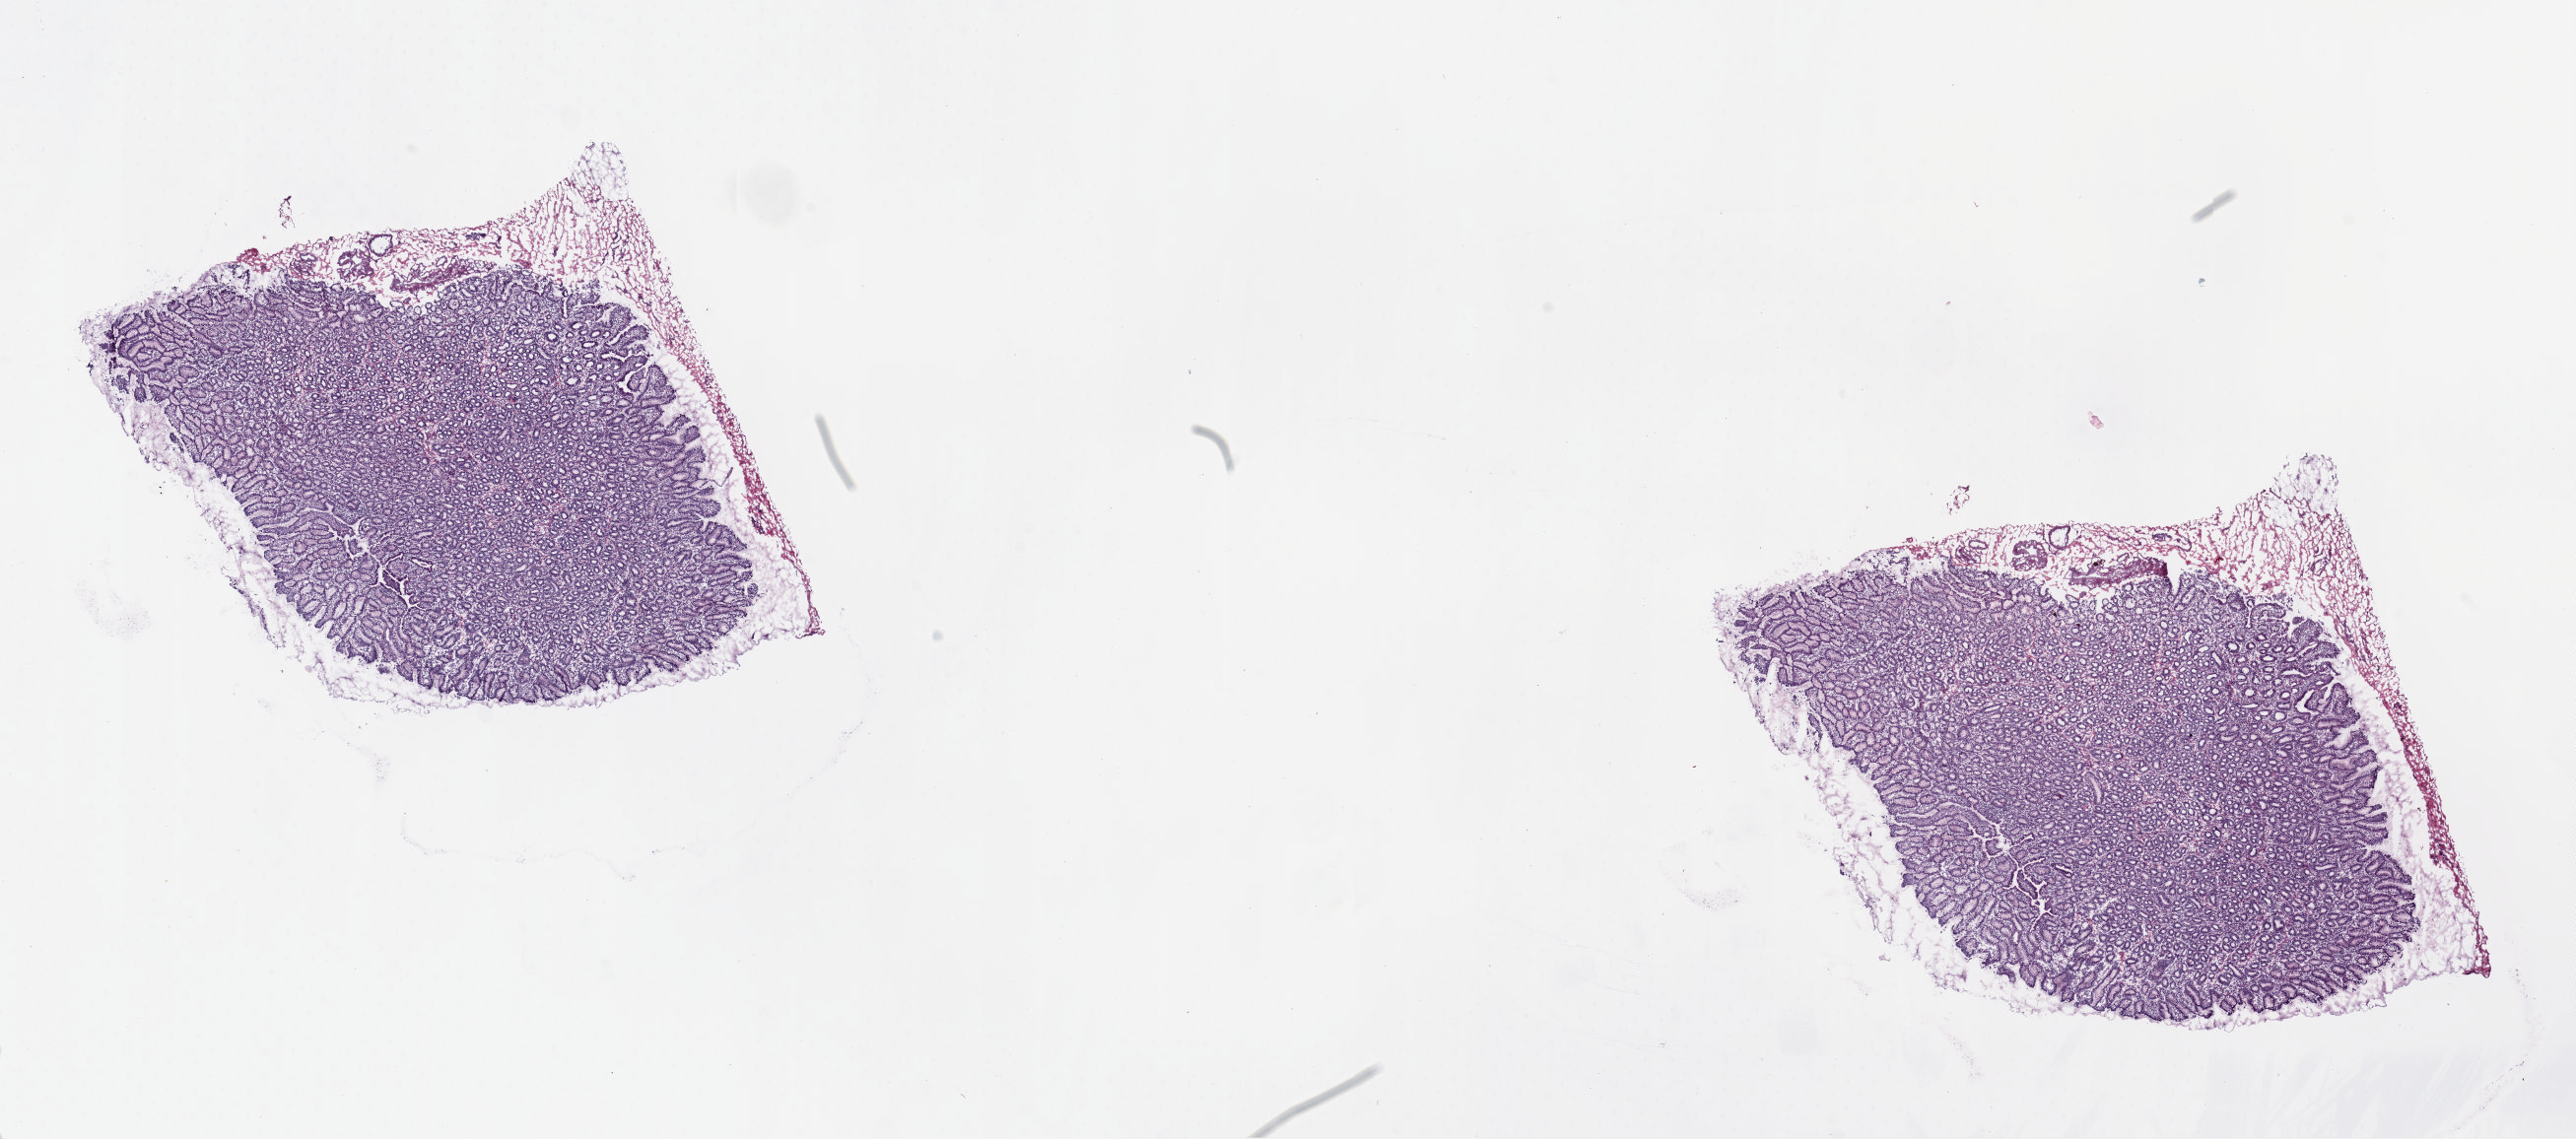
Whole-slide histology image, H&E, shown as a low-resolution overview of the whole scanned area (about 20.6 x 9.1 mm), frozen section, stomach, solid tissue normal (non-tumour tissue) sample. Male, age 72 years at initial diagnosis. Composition of this section per pathologist review: tumour cells 0%, tumour nuclei 0%, normal cells 100%, stromal cells 0%, necrosis 0%. Inflammatory infiltration, as recorded: lymphocyte infiltration 2%, monocyte infiltration 1%, neutrophil infiltration 0%.
This section: solid tissue normal (non-tumour) sample from the same patient. Patient diagnosis: Carcinoma, diffuse type (body of stomach).